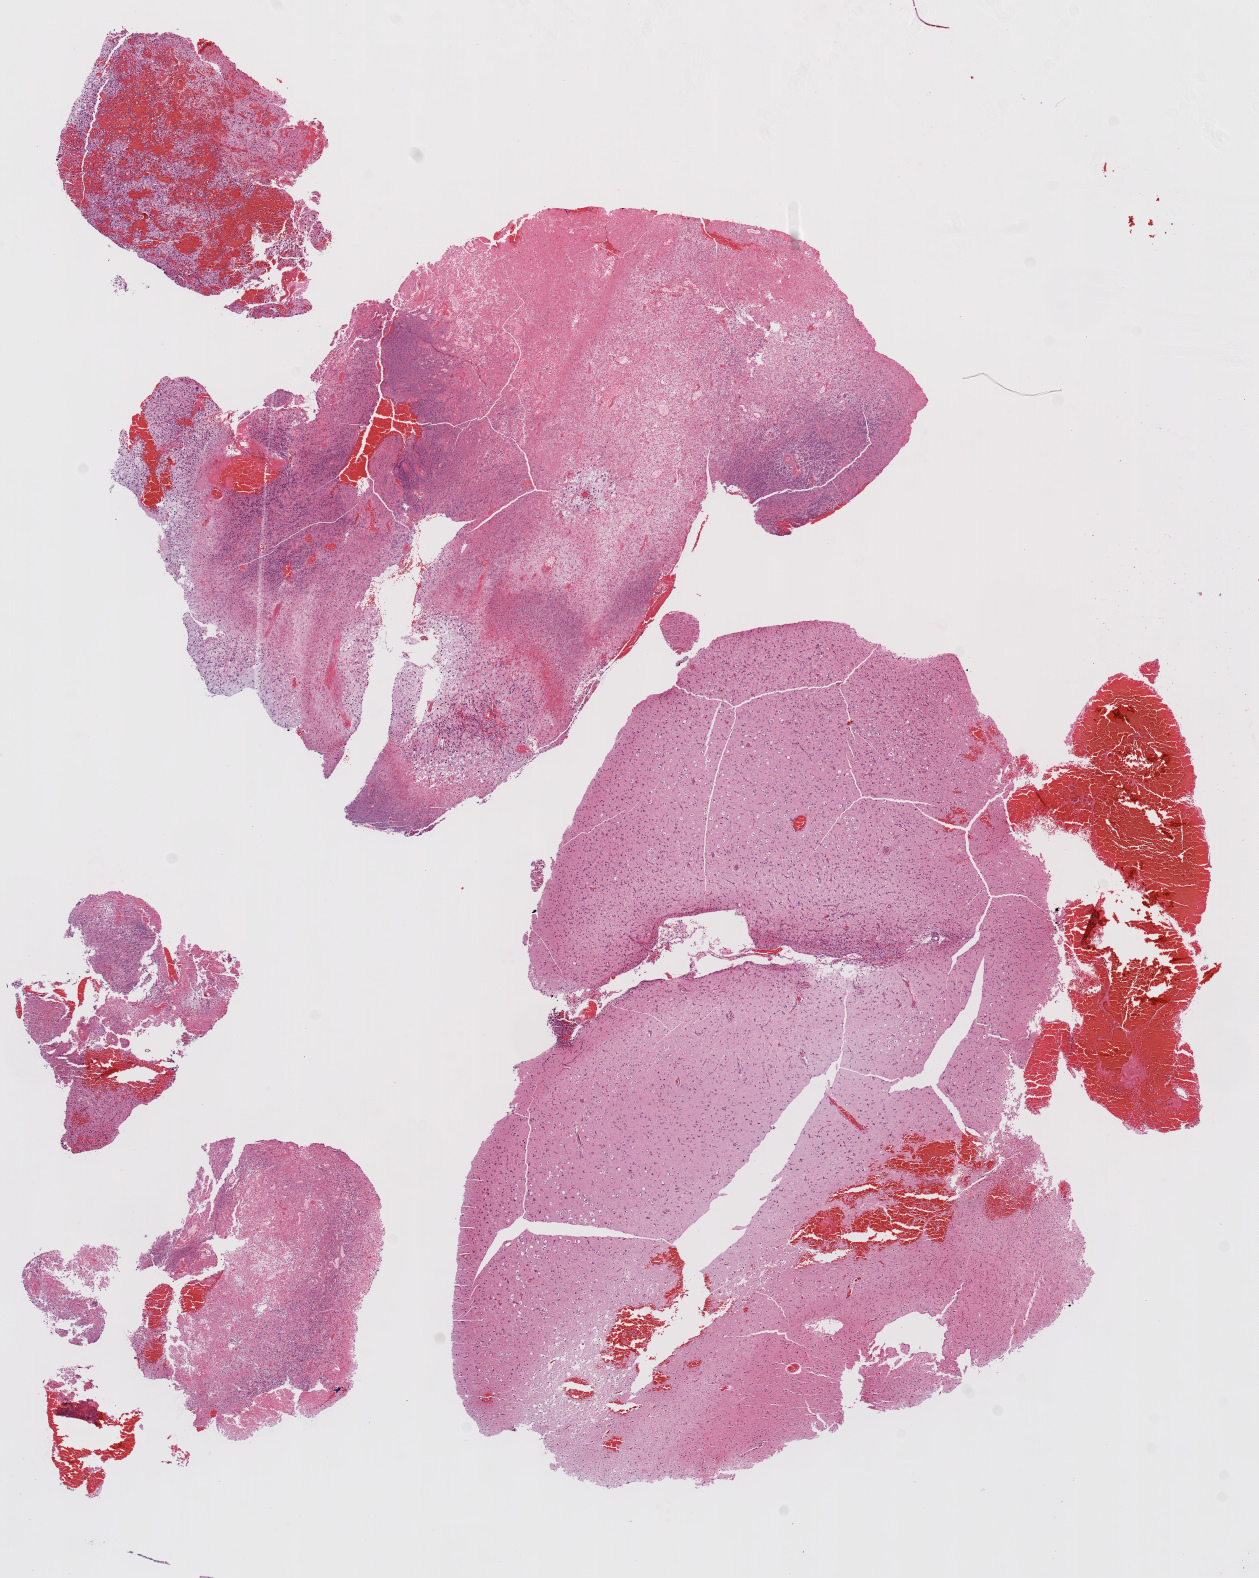
H&E whole-slide image — a low-resolution overview of the entire scanned area, about 10.2 x 12.7 mm (from a 20x scan), formalin-fixed paraffin-embedded (FFPE) diagnostic section, sample: primary tumour, brain. Patient: male, age at initial diagnosis 54 years.
Diagnosis: Glioblastoma.